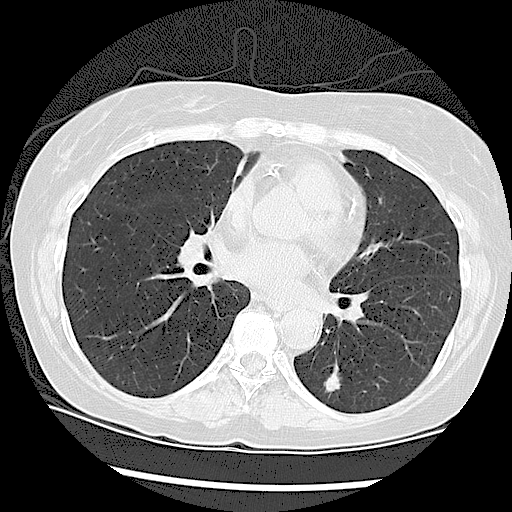
Low-dose screening chest CT, one axial slice; slice 50 of 108 in the series (ordered by position); reconstruction kernel LUNG; lung window (W 1500 / L -600 HU); 2.5 mm slice thickness; 512 × 512 image matrix, field of view 330 × 330 mm.
Structures marked on this image (outlined manually by an expert reader):
- lesion 1 (tumor, lower lobe of left lung): box from (x=325, y=361) to (x=341, y=394) px